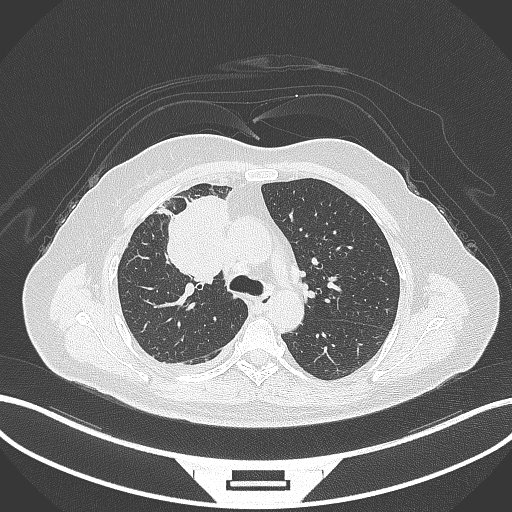
Chest CT, one axial slice. Slice 190 of 305 in the series (ordered by position). Lung window (W 1500 / L -600 HU). 1 mm slice thickness. 512 × 512 image matrix. Female patient, age 52 years. Case-level facts recorded for this patient, not image findings: clinical TNM (as recorded): T3 N1 M1.
Annotated regions visible in this slice (rectangle marked by the reading radiologist):
- lung tumour (recorded histology: adenocarcinoma): bounding box [x1, y1, x2, y2] px = [163, 190, 231, 289]